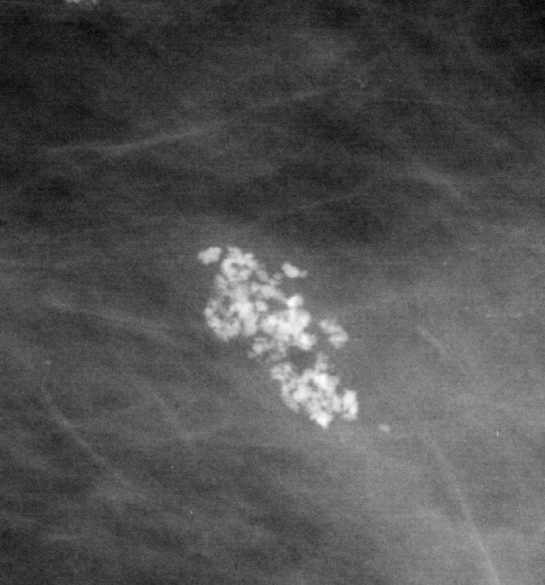
Cropped region of a digitized screen-film mammogram centred on a radiologist-marked abnormality, left breast, MLO view.
Marked abnormality: calcifications, morphology pleomorphic, distribution clustered; BI-RADS assessment category 4; pathology (as recorded): benign.